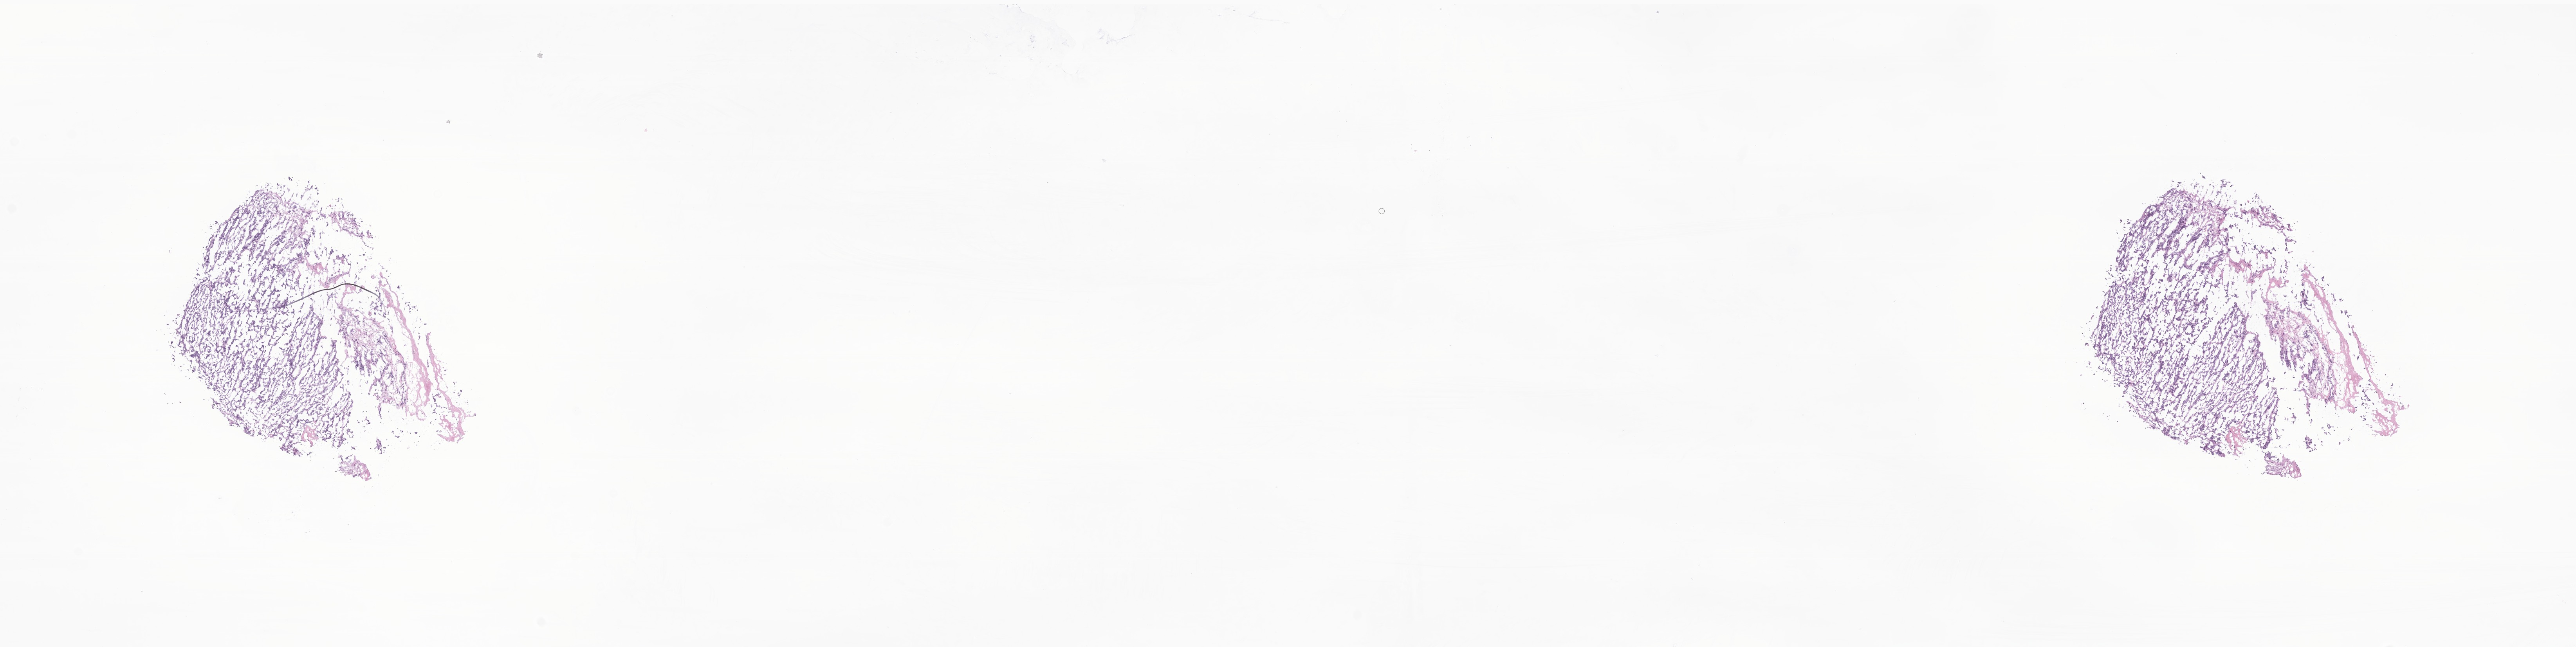
Digitized hematoxylin and eosin (H&E)-stained section of tumor tissue from the thyroid, a low-resolution overview of the entire scanned area, about 27.7 x 7.0 mm, cryosection (OCT / tissue freezing medium). Female patient, age 185 months.
Diagnosis: Papillary carcinoma, NOS.